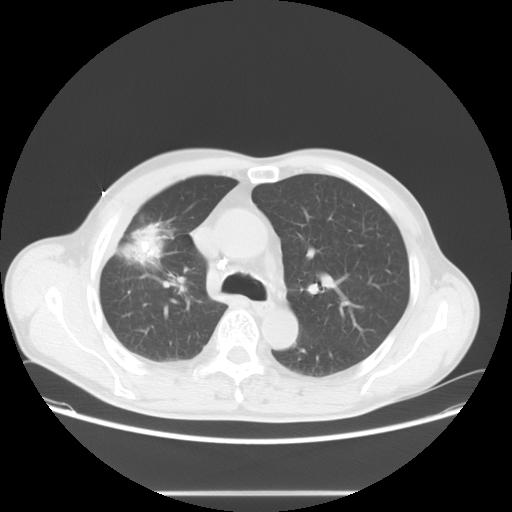
Chest CT, one axial slice. Slice 47 of 71 in the series (ordered by position). 120 kVp. Lung window (W 1500 / L -600 HU). 512 × 512 image matrix, field of view 392 × 392 mm. Male patient, age 67 years. From the clinical record (not read from this slice): clinical TNM (as recorded): T2 N0 M0.
Outlined on this slice (bounding box drawn by a radiologist):
- lung tumour (recorded histology: adenocarcinoma): box from (x=128, y=219) to (x=166, y=265) px